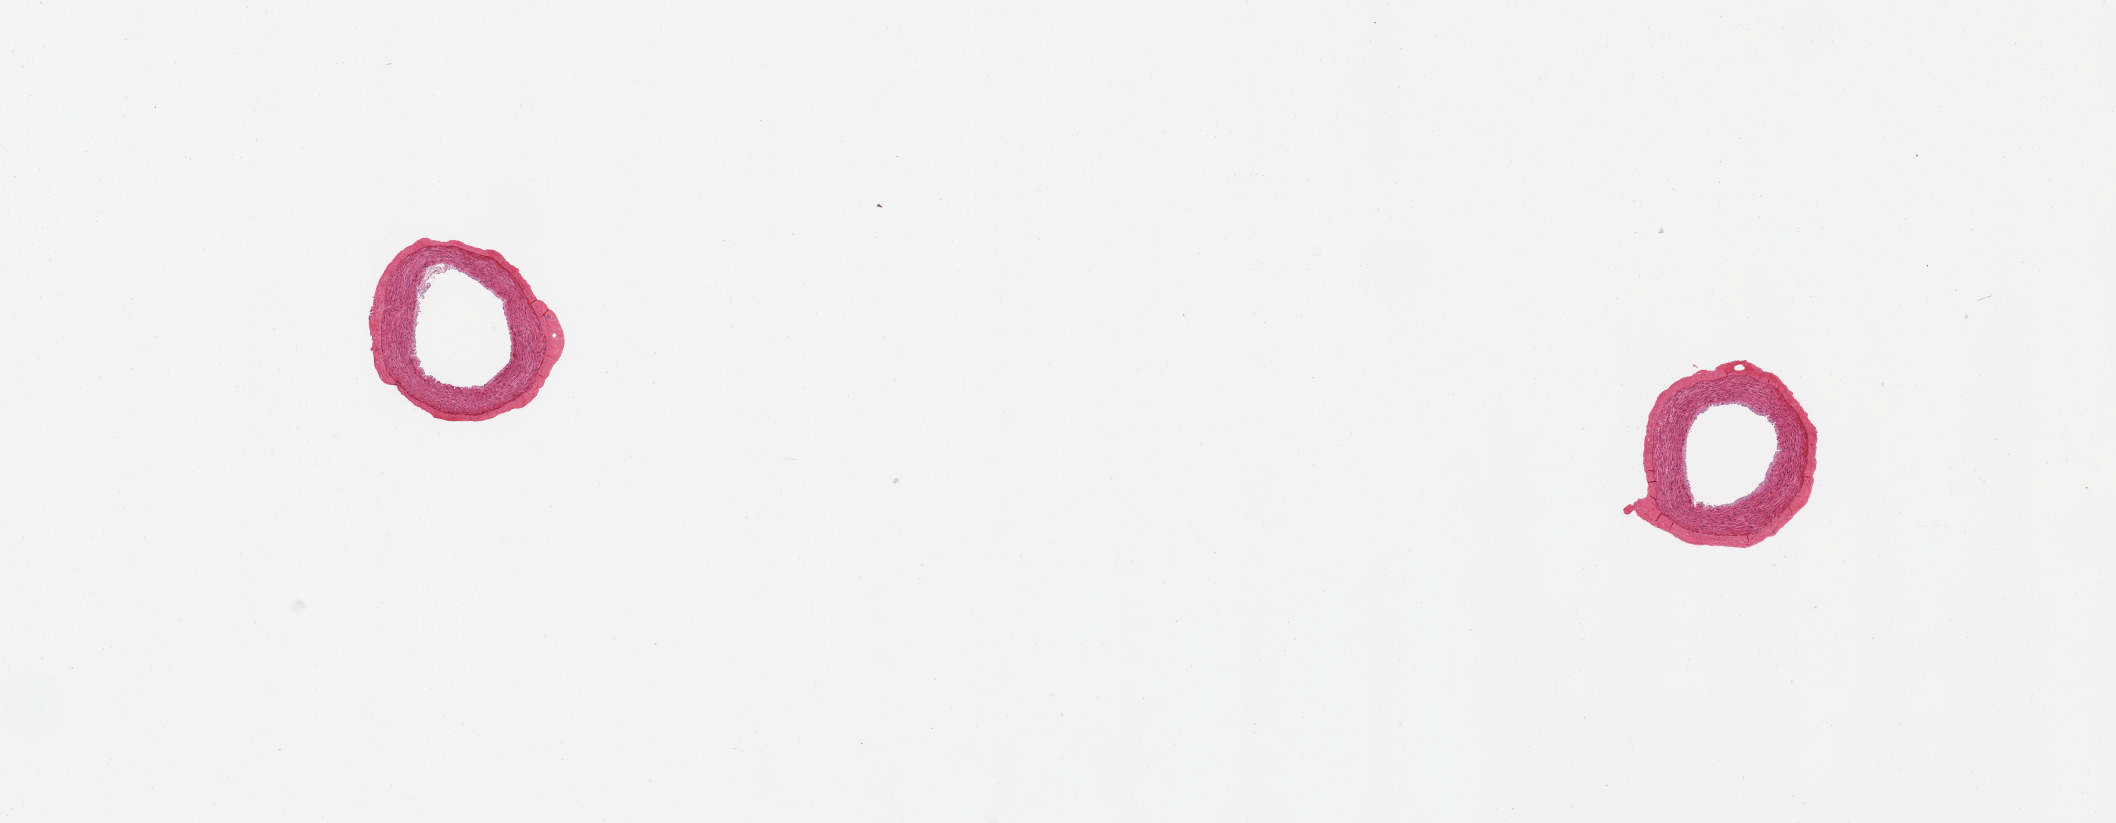
Haematoxylin and eosin whole-slide image — a low-resolution overview of the entire scanned area, about 16.7 x 6.5 mm (from a 20x scan); PAXgene-fixed, paraffin-embedded tissue; sampled site (target tissue): tibial artery; tissue donor sample. Female donor.
Pathologist's review note for this sample: 2 pieces; well dissected, lesion free.